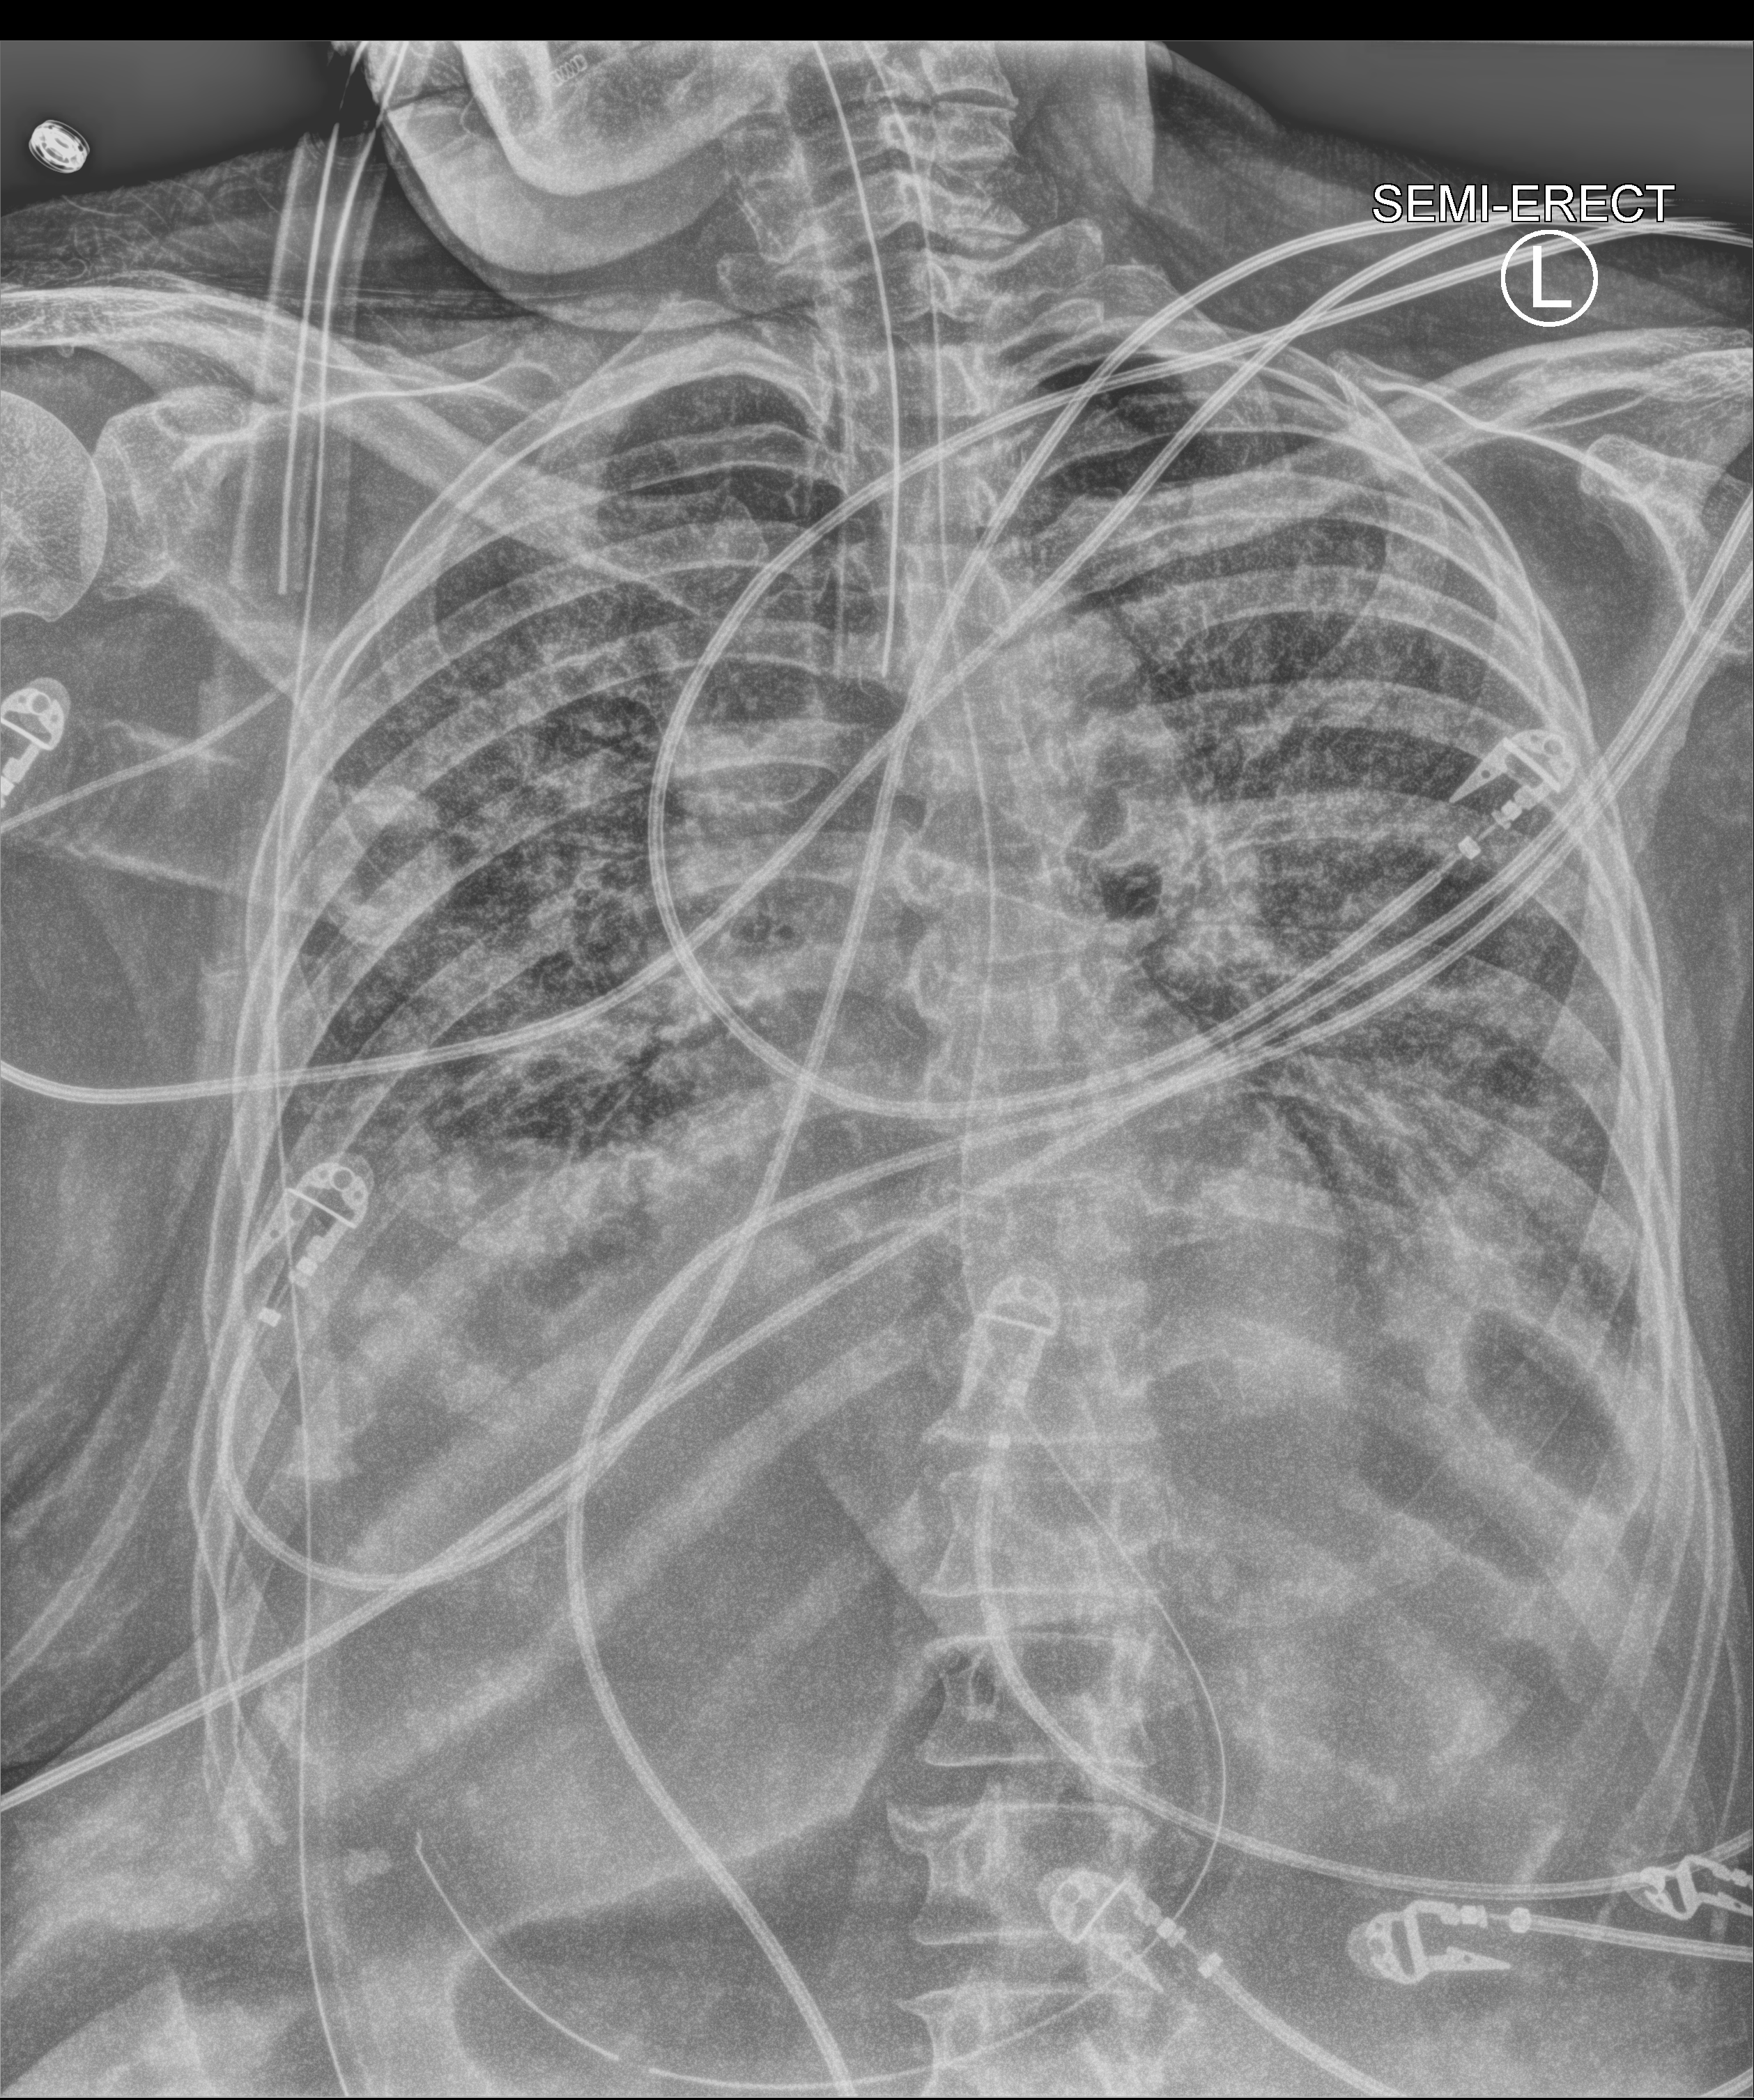
Chest X-ray (portable); anteroposterior (AP) projection. Female patient hospitalised with COVID-19, age 75–90 years.
From the hospital-stay record, not from the radiograph (when in the stay this image was taken is not recorded):
- diabetes (admission record): yes
- other chronic lung disease (admission record): no